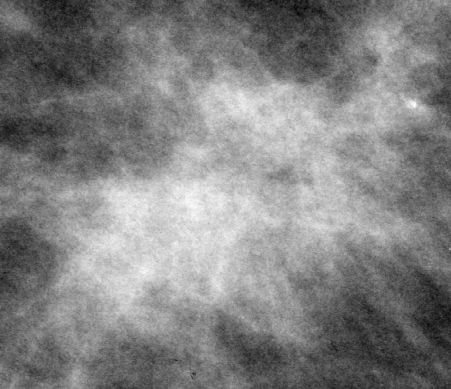
Cropped region of a digitized screen-film mammogram centred on a radiologist-marked abnormality; left breast; MLO view.
Finding: mass, shape irregular, margins spiculated; BI-RADS assessment category 5; subtlety rating 5 on a 1 (subtle) to 5 (obvious) scale; pathology result (as recorded, not read from the image): malignant.